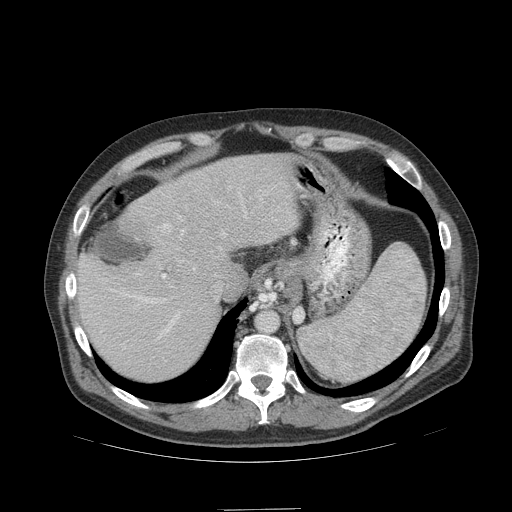
Contrast-enhanced abdominal CT (liver protocol), one axial slice; position 79 of 99 along the scan axis; reconstruction kernel STANDARD; soft-tissue window (W 400 / L 40 HU); 2.5 mm slice thickness; 512 × 512 image matrix. Case-level facts recorded for this patient, not image findings: diagnosis: hepatocellular carcinoma (patient treated with transarterial chemoembolisation; whether this scan precedes or follows treatment is not stated here); TNM stage (as recorded): Stage-I; Child-Pugh class: A; tumour nodularity: uninodular; tumour size: 3.6 cm.
Outlined on this slice (semi-automatically segmented with operator editing):
- liver parenchyma outside the tumour (the mass and vessels are separate outlines, so this box may not span the whole liver): box from (x=76, y=154) to (x=298, y=380) px
- liver vessels: (x=92, y=190)–(x=266, y=339)